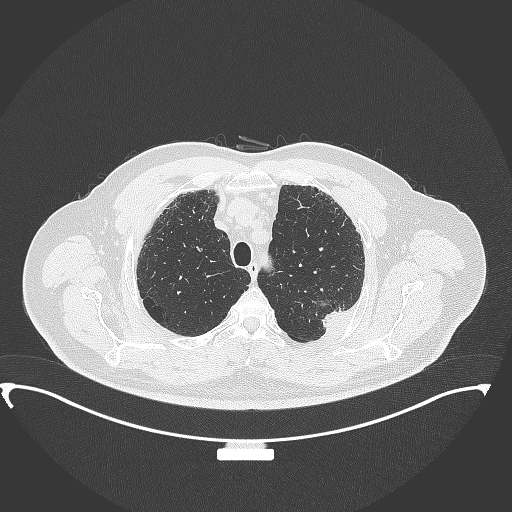
Chest CT, one axial slice. Slice 294 of 350 in the series (ordered by position). 120 kVp. Lung window (W 1500 / L -600 HU). 1 mm slice thickness. 512 × 512 image matrix, field of view 459 × 459 mm. Patient: male, 64 years. Case-level facts recorded for this patient, not image findings: clinical TNM (as recorded): T1c N1 M1.
Structures marked on this image (bounding box drawn by a radiologist):
- lung tumour (recorded histology: adenocarcinoma): box from (x=316, y=302) to (x=352, y=334) px